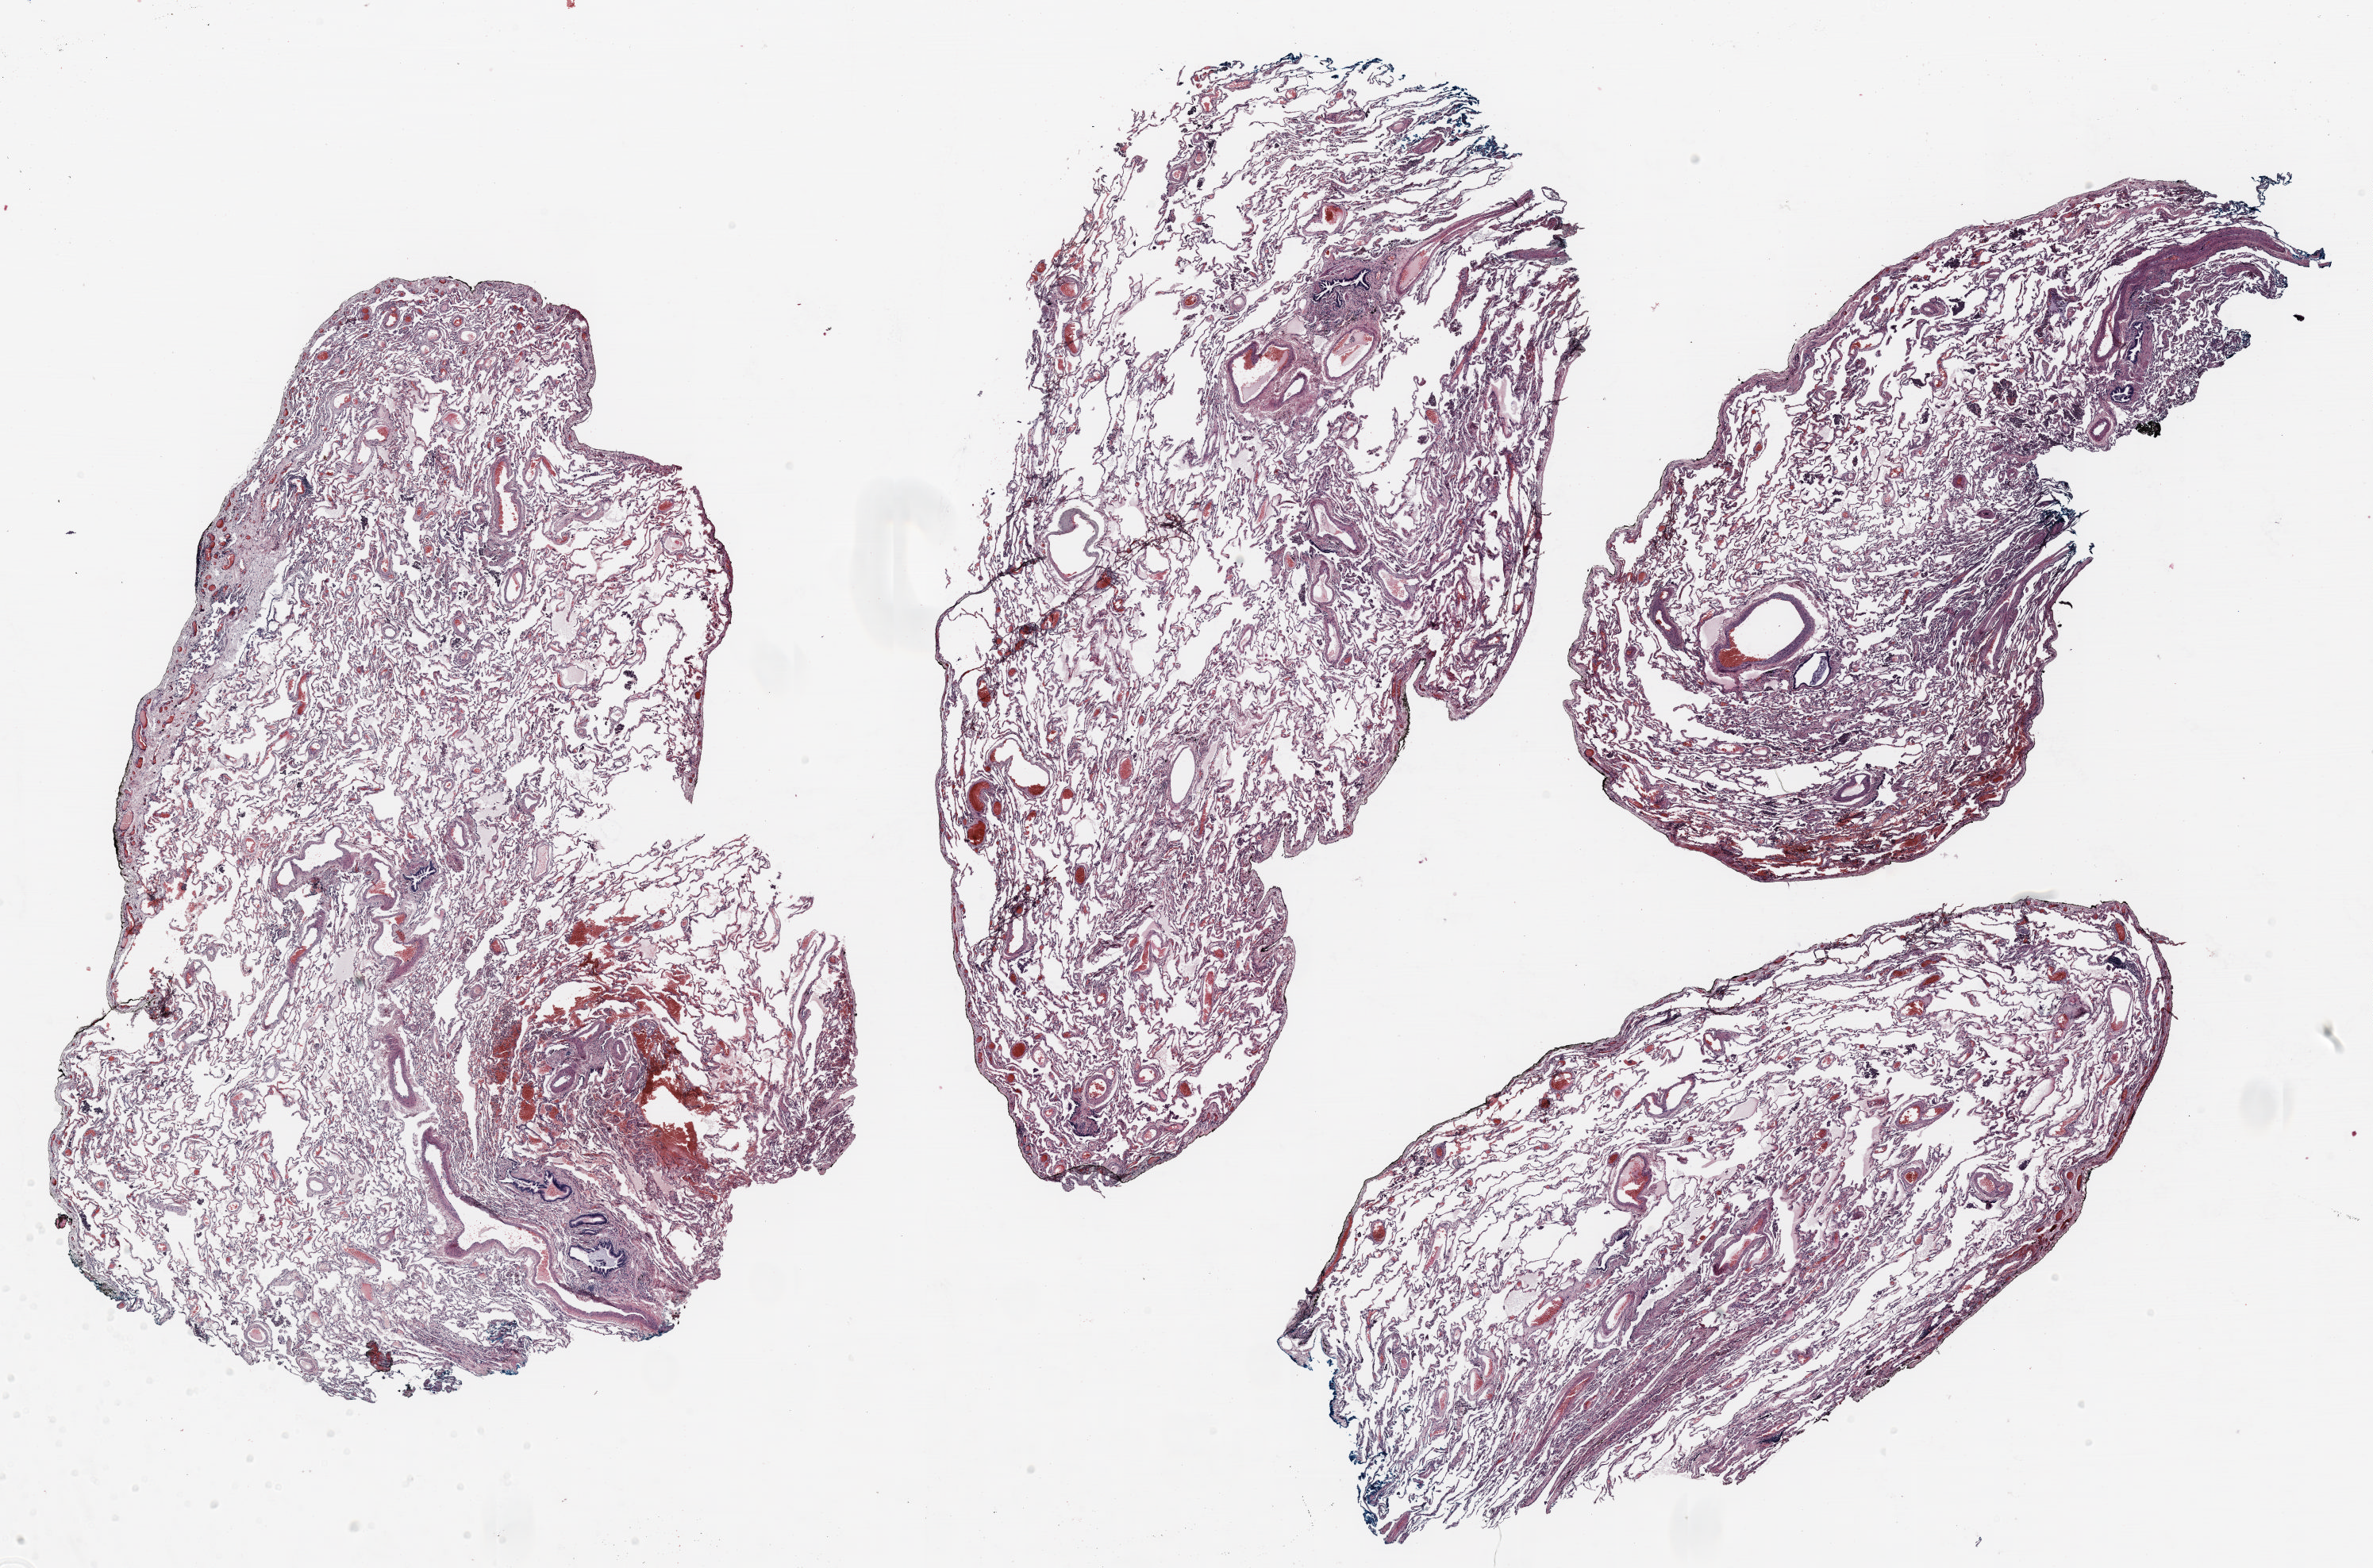
H&E-stained whole-slide image — low-resolution overview of the scanned area, about 24.0 x 15.9 mm. FFPE section. Lung tissue. Female patient, aged 66 at enrolment. Grade: moderately differentiated (G2).
• participant's lung-cancer diagnosis: Adenocarcinoma, NOS
• tumour size (pathology): 17 mm
• primary tumour location (clinical record): left upper lobe
• stage (AJCC 6th edition): IB
• note: participant had 2 primary lung cancers recorded; fields above describe the first